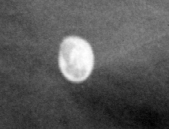
Region of interest cut from a scanned film mammogram (one marked finding), left breast, MLO view, BI-RADS breast density category 4 (scale 1–4).
Calcifications, morphology round and regular / lucent center / punctate, distribution diffusely scattered; BI-RADS assessment category 2; subtlety rating 5 on a 1 (subtle) to 5 (obvious) scale; benign; no additional work-up was recommended (benign without callback).